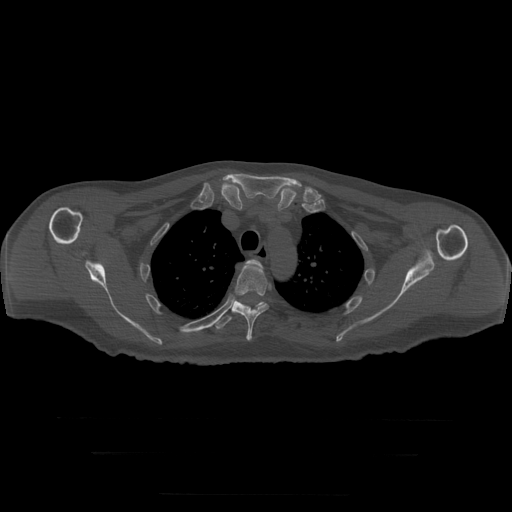
CT including the spine, one axial slice; slice 239 of 397 in the series (ordered by position); bone window (W 1800 / L 400 HU); 512 × 512 image matrix, field of view 510 × 510 mm. Patient age 73 years. Case-level facts recorded for this patient, not image findings: primary cancer: prostate.
Annotated regions visible in this slice (semi-automatic segmentation, software-assisted and operator-edited):
- T3 vertebra: bounding box <246,260,262,266> (left, top, right, bottom; pixels)
- T4 vertebra: <234,263,269,341>
- T5 vertebra: <215,300,264,330>